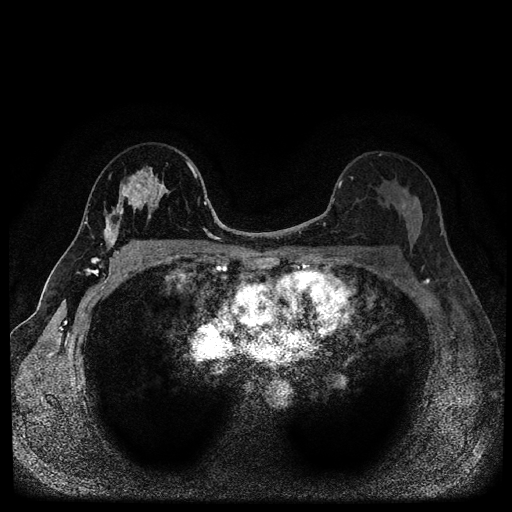
Breast MRI (dynamic contrast-enhanced, multi-phase), one axial slice. Position 63 of 116 along the scan axis. Dynamic contrast-enhanced series, time point 2 of 5 at this slice position (early post-contrast). 1.5 T. TE 2.7 ms, TR 5.4 ms. 512 × 512 image matrix, field of view 320 × 320 mm. Female patient, age 49 years.
Annotated regions visible in this slice (semi-automatic segmentation, software-assisted and operator-edited):
- breast lesion (labelled benign in the annotation): box from (x=102, y=166) to (x=172, y=253) px